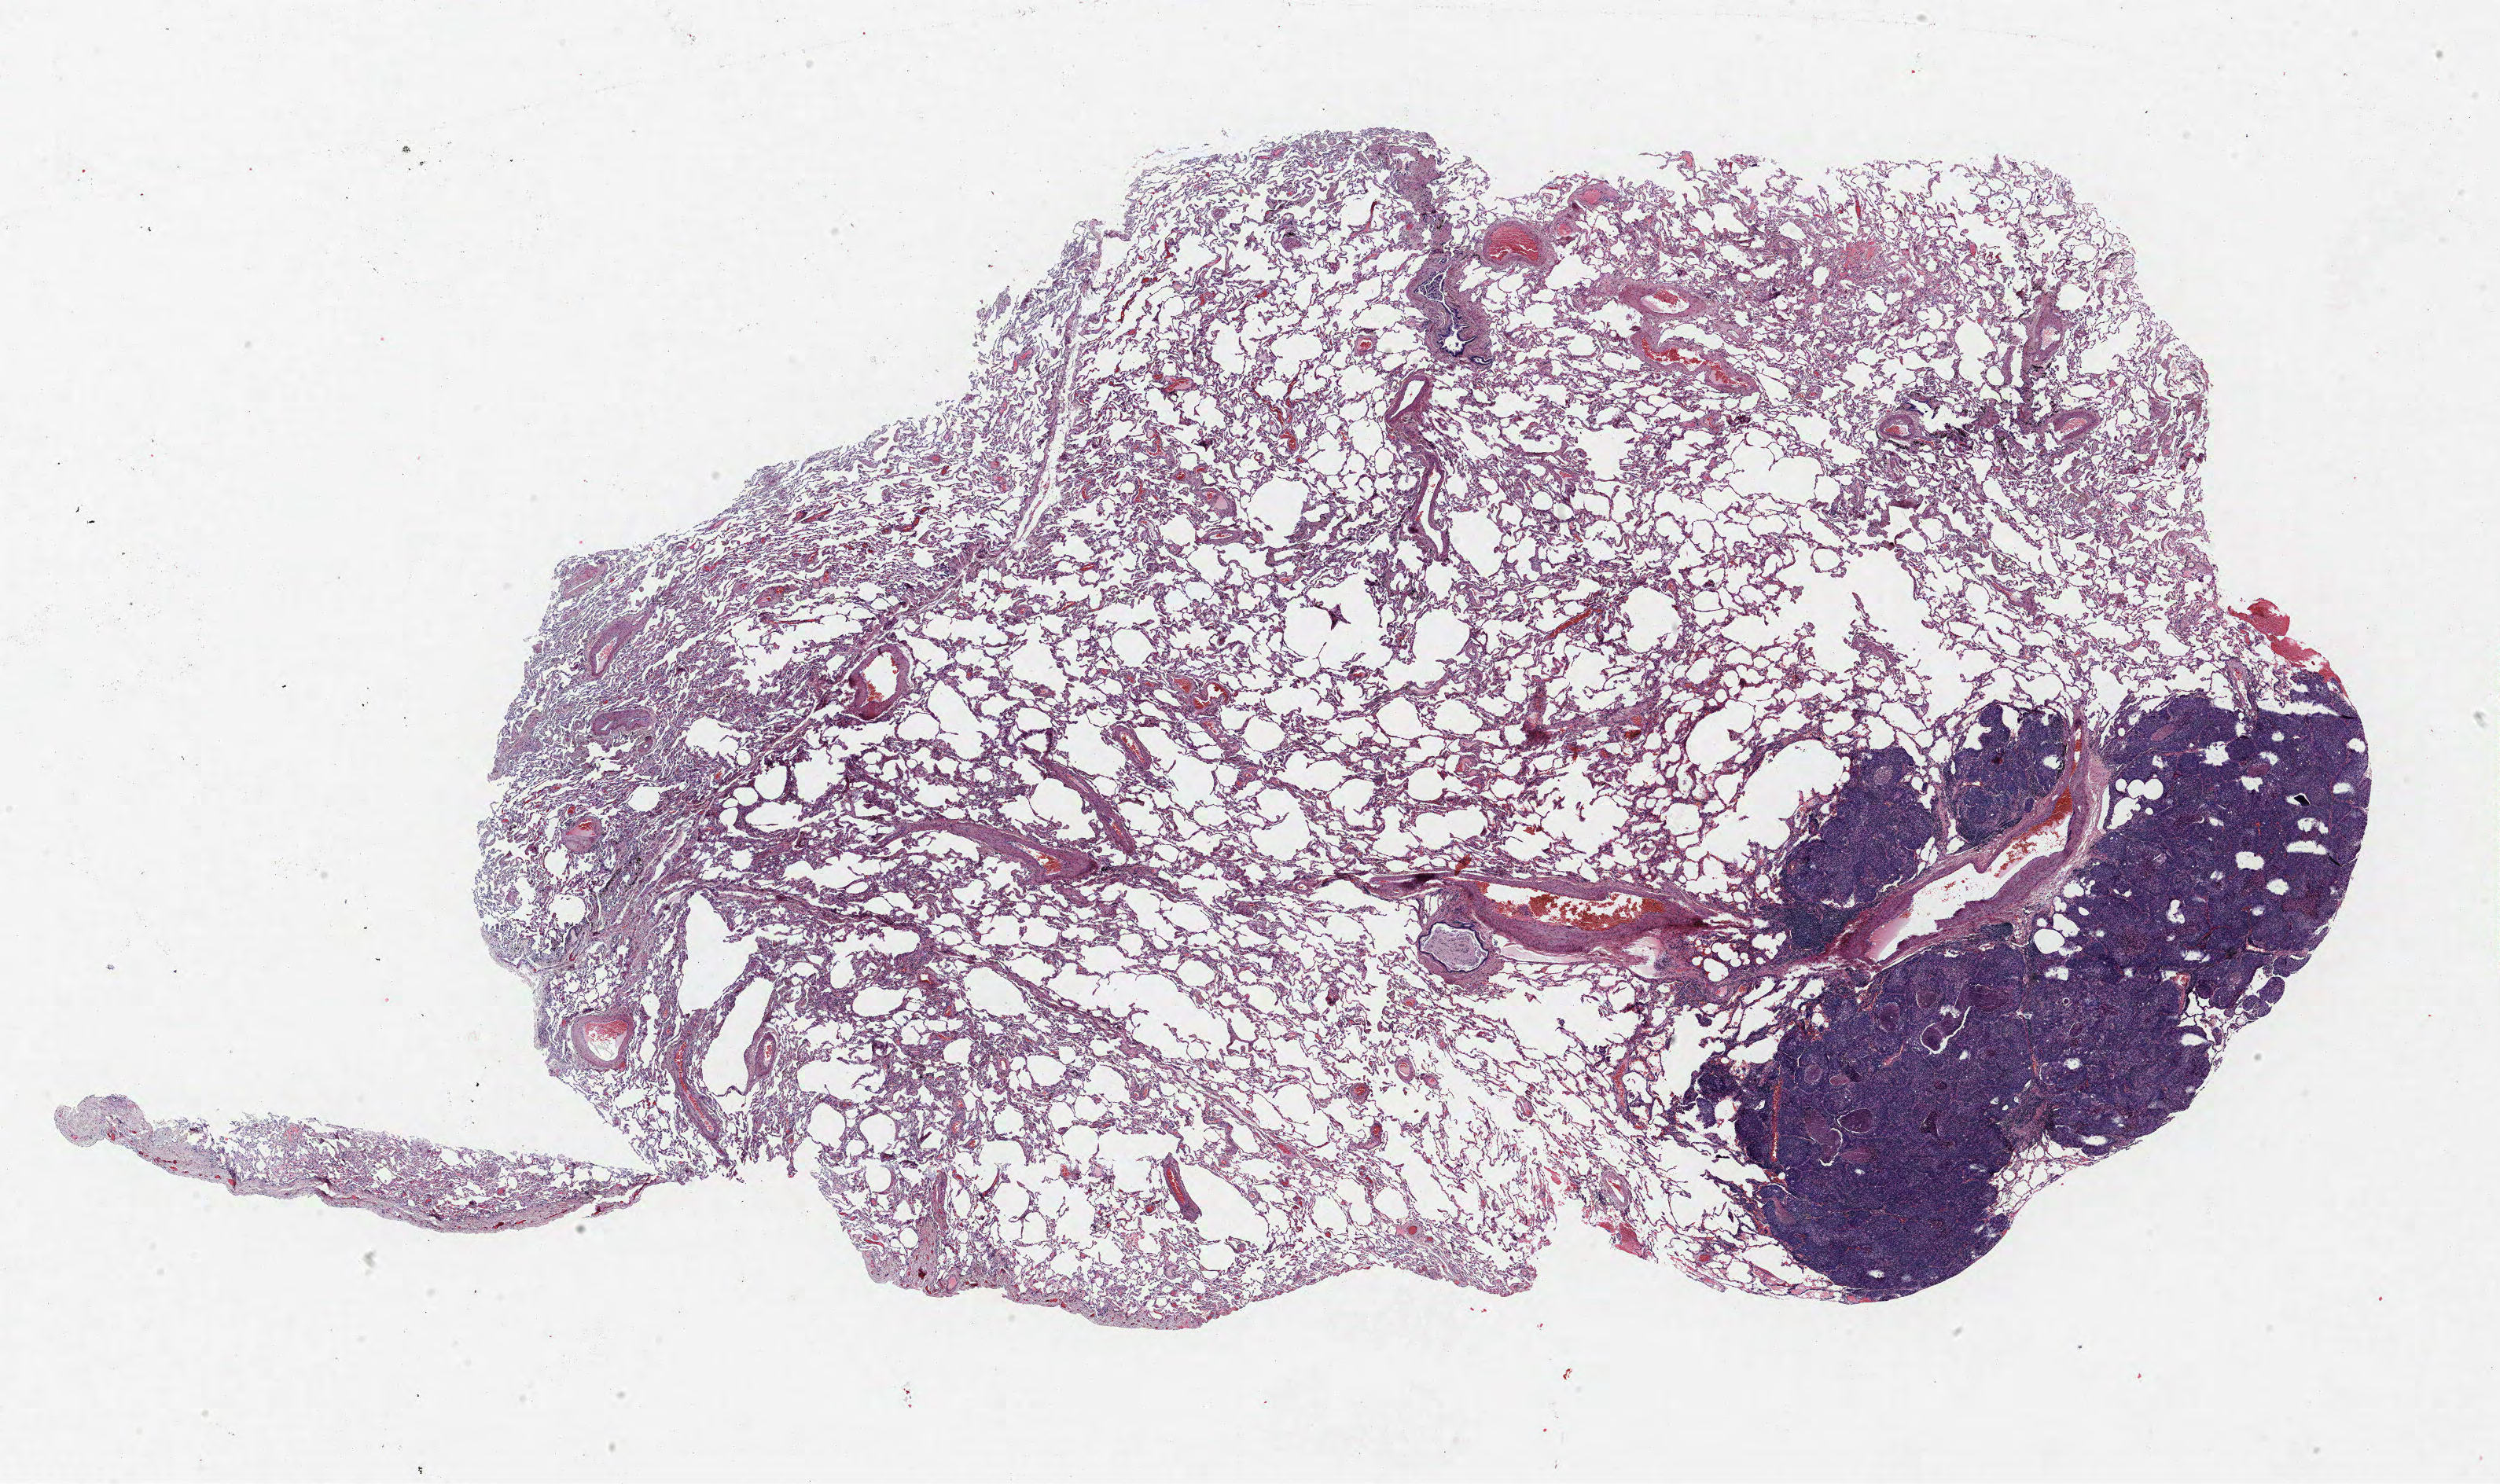
Whole-slide histology image, H&E-stained, whole scanned area (about 25.4 x 15.1 mm) shown as a low-resolution overview. Formalin-fixed paraffin-embedded (FFPE) section. Lung. Male, age 64 at enrolment. Grade: poorly differentiated (G3).
Participant's lung-cancer diagnosis: Squamous cell carcinoma, NOS. Tumour size (pathology): 14 mm. Primary tumour location (clinical record): left upper lobe. Stage (AJCC 6th edition): IA.